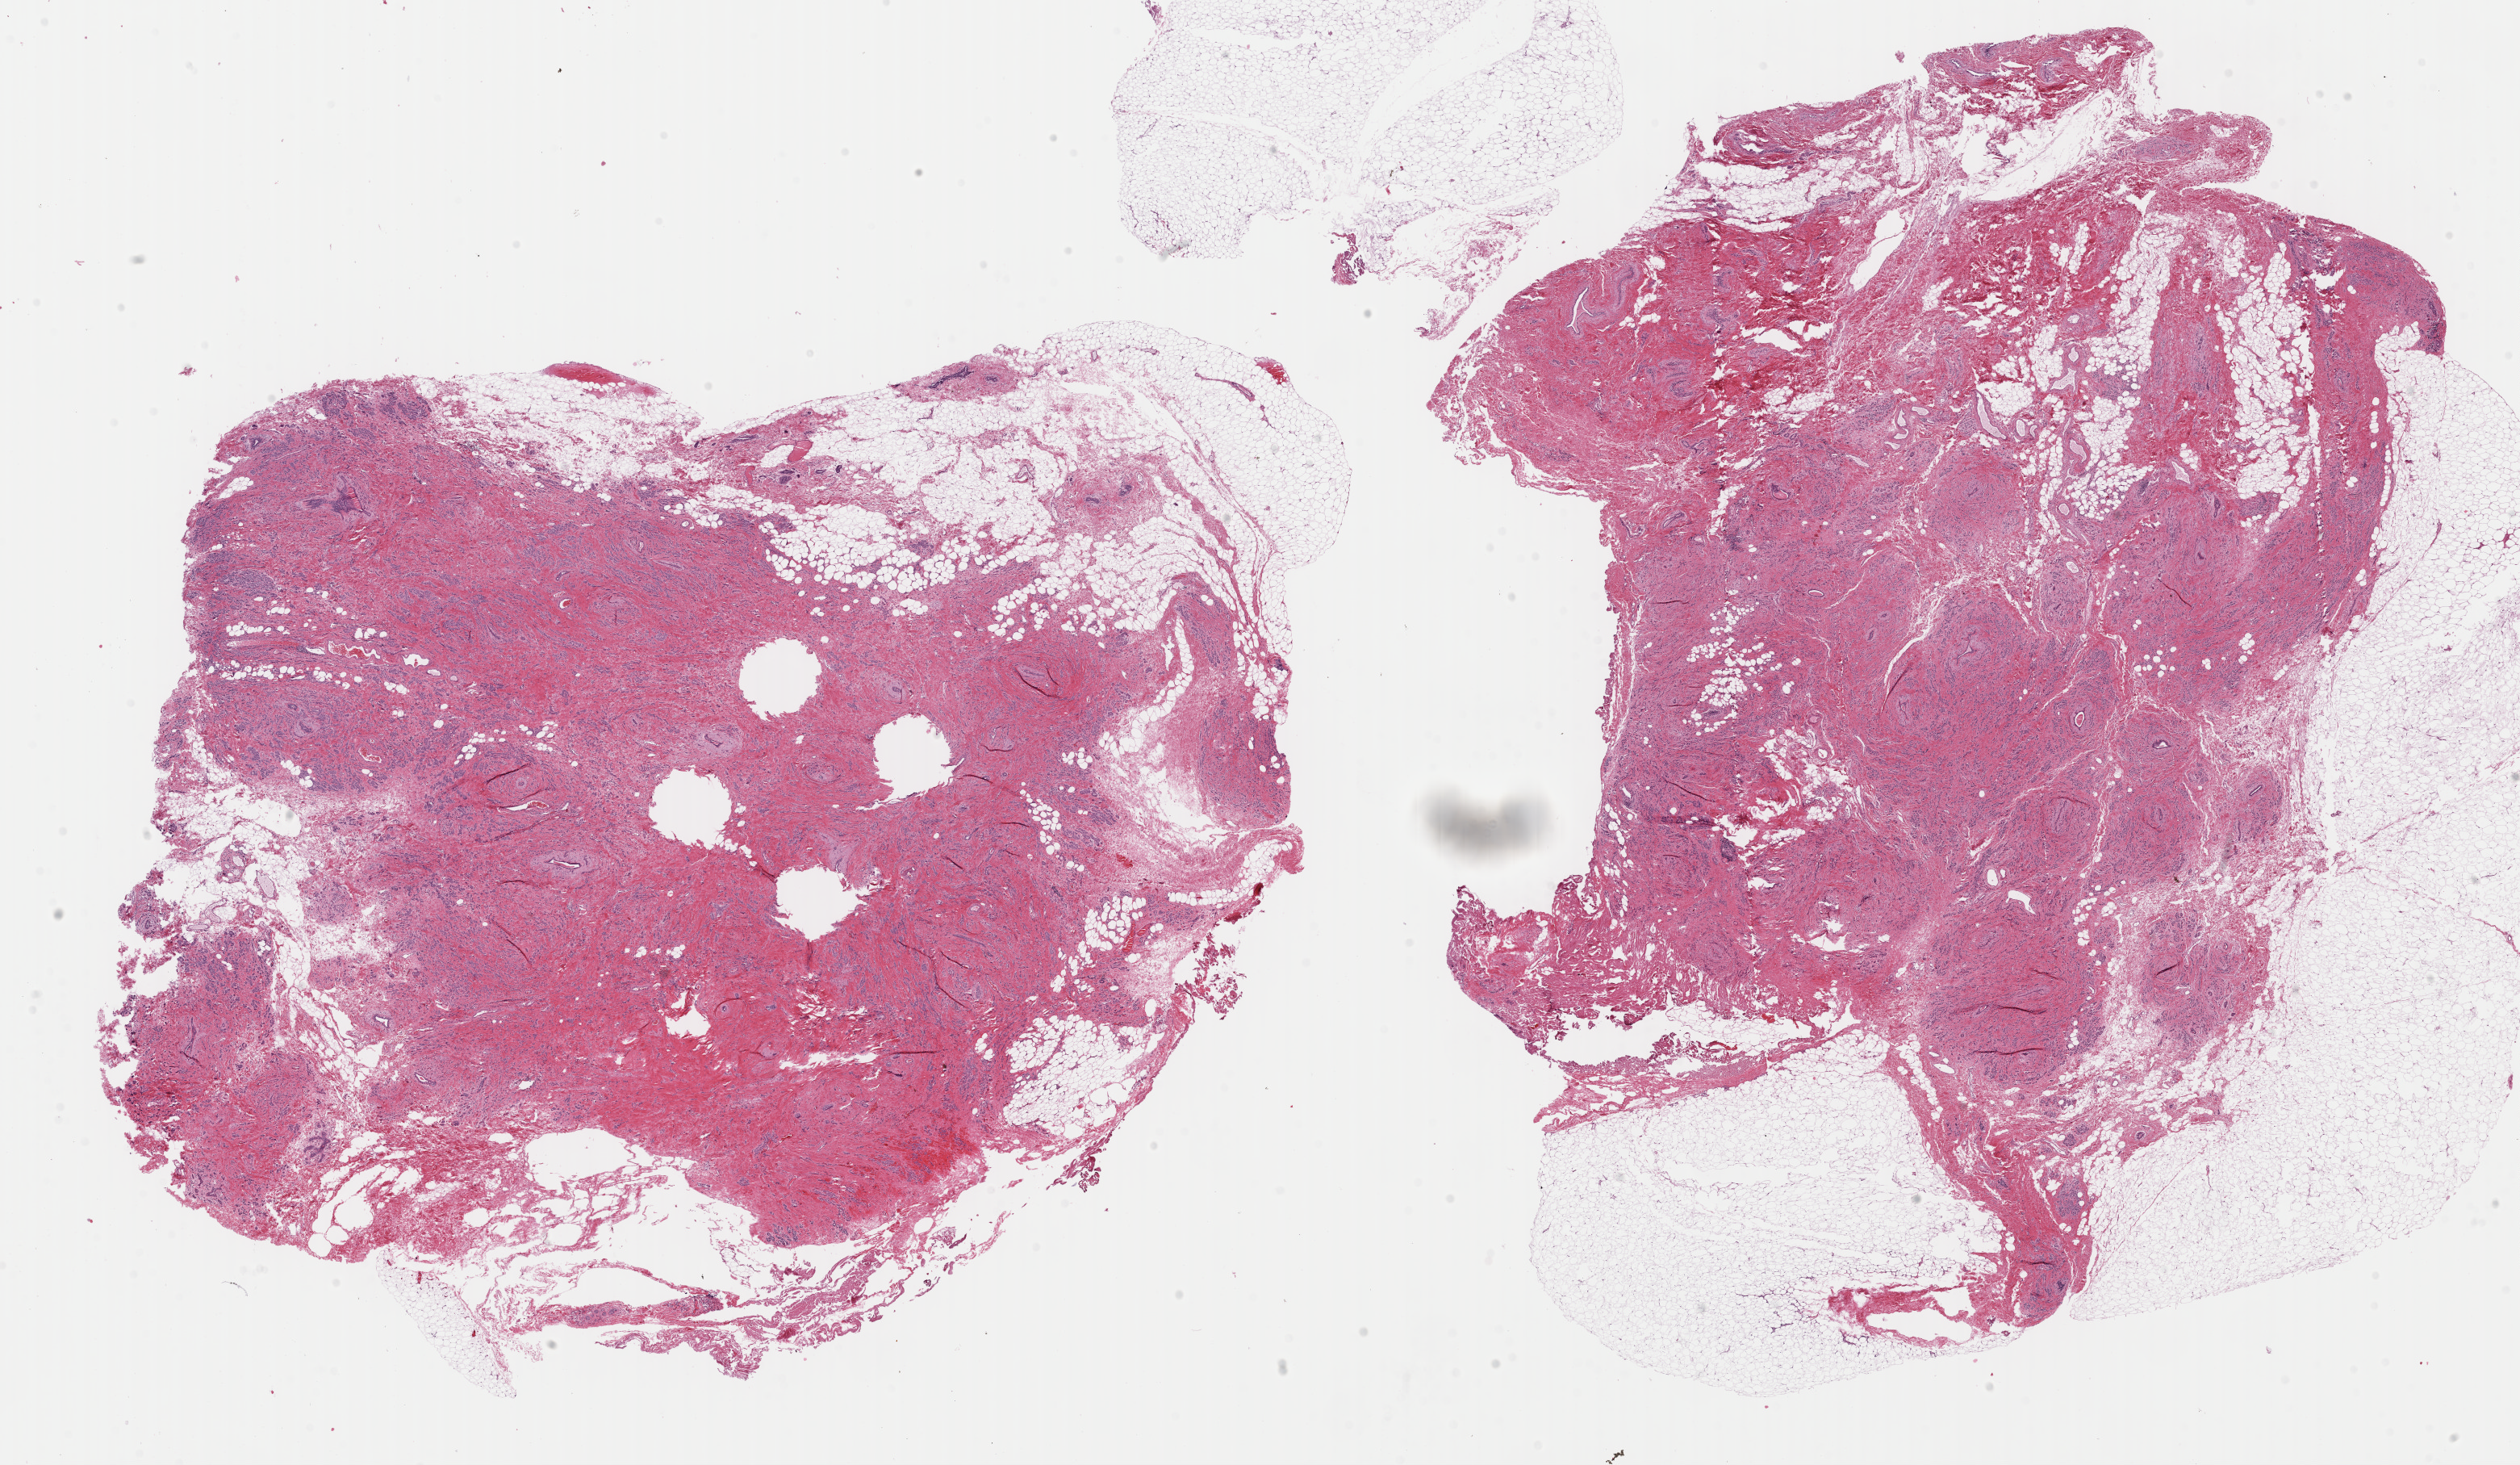
Whole-slide histology image, Hematoxylin and eosin (H&E) stained, whole scanned area (about 24.7 x 14.3 mm) shown as a low-resolution overview. Formalin-fixed paraffin-embedded (FFPE) diagnostic section. Breast, primary tumour sample. Patient: female, age at initial diagnosis 43 years.
TNM: T3 N2 M0. Lymph nodes positive (case pathology): 7 of 19 examined. Diagnosis: Infiltrating duct and lobular carcinoma. AJCC pathologic stage: IIIA.